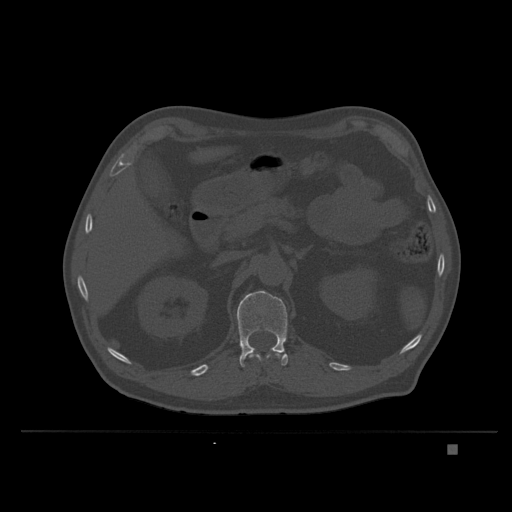
CT including the spine, one axial slice; position 144 of 435 along the scan axis; bone window (W 1800 / L 400 HU); 1.5 mm slice thickness; 512 × 512 image matrix, field of view 434 × 434 mm. Male patient, age 73 years. Case-level facts recorded for this patient, not image findings: primary cancer: skin.
Annotated regions visible in this slice (semi-automatically segmented with operator editing):
- L1 vertebra: bounding box <237,290,288,367> (left, top, right, bottom; pixels)
- T12 vertebra: <249,350,281,361>